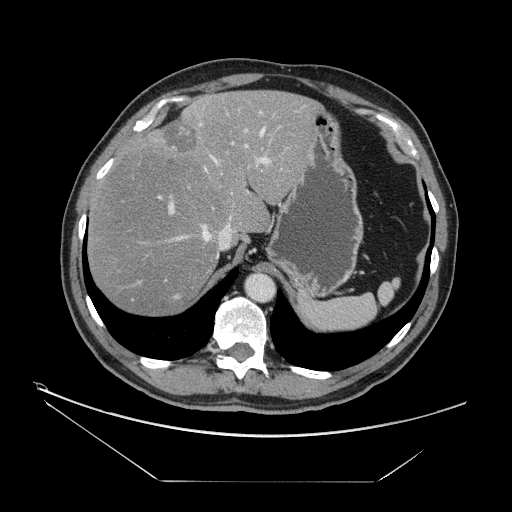
Contrast-enhanced abdominal CT, one axial slice; slice 116 of 161 in the series (ordered by position); 120 kVp; intravenous contrast given; soft-tissue window (W 400 / L 40 HU); 2.5 mm slice thickness; 512 × 512 image matrix, field of view 440 × 440 mm. Male patient, age 65 years. Case-level facts recorded for this patient, not image findings: diagnosis: colorectal cancer liver metastases, imaged before liver resection; multiple liver metastases: yes.
Structures marked on this image (manually delineated by an expert):
- hepatic veins: bounding box <175,128,265,257> (left, top, right, bottom; pixels)
- liver: <88,91,318,317>
- planned liver remnant (the part of the liver to remain after resection): <88,91,317,316>
- portal vein (with intrahepatic branches): <158,106,305,219>
- liver metastasis: <160,117,197,155>